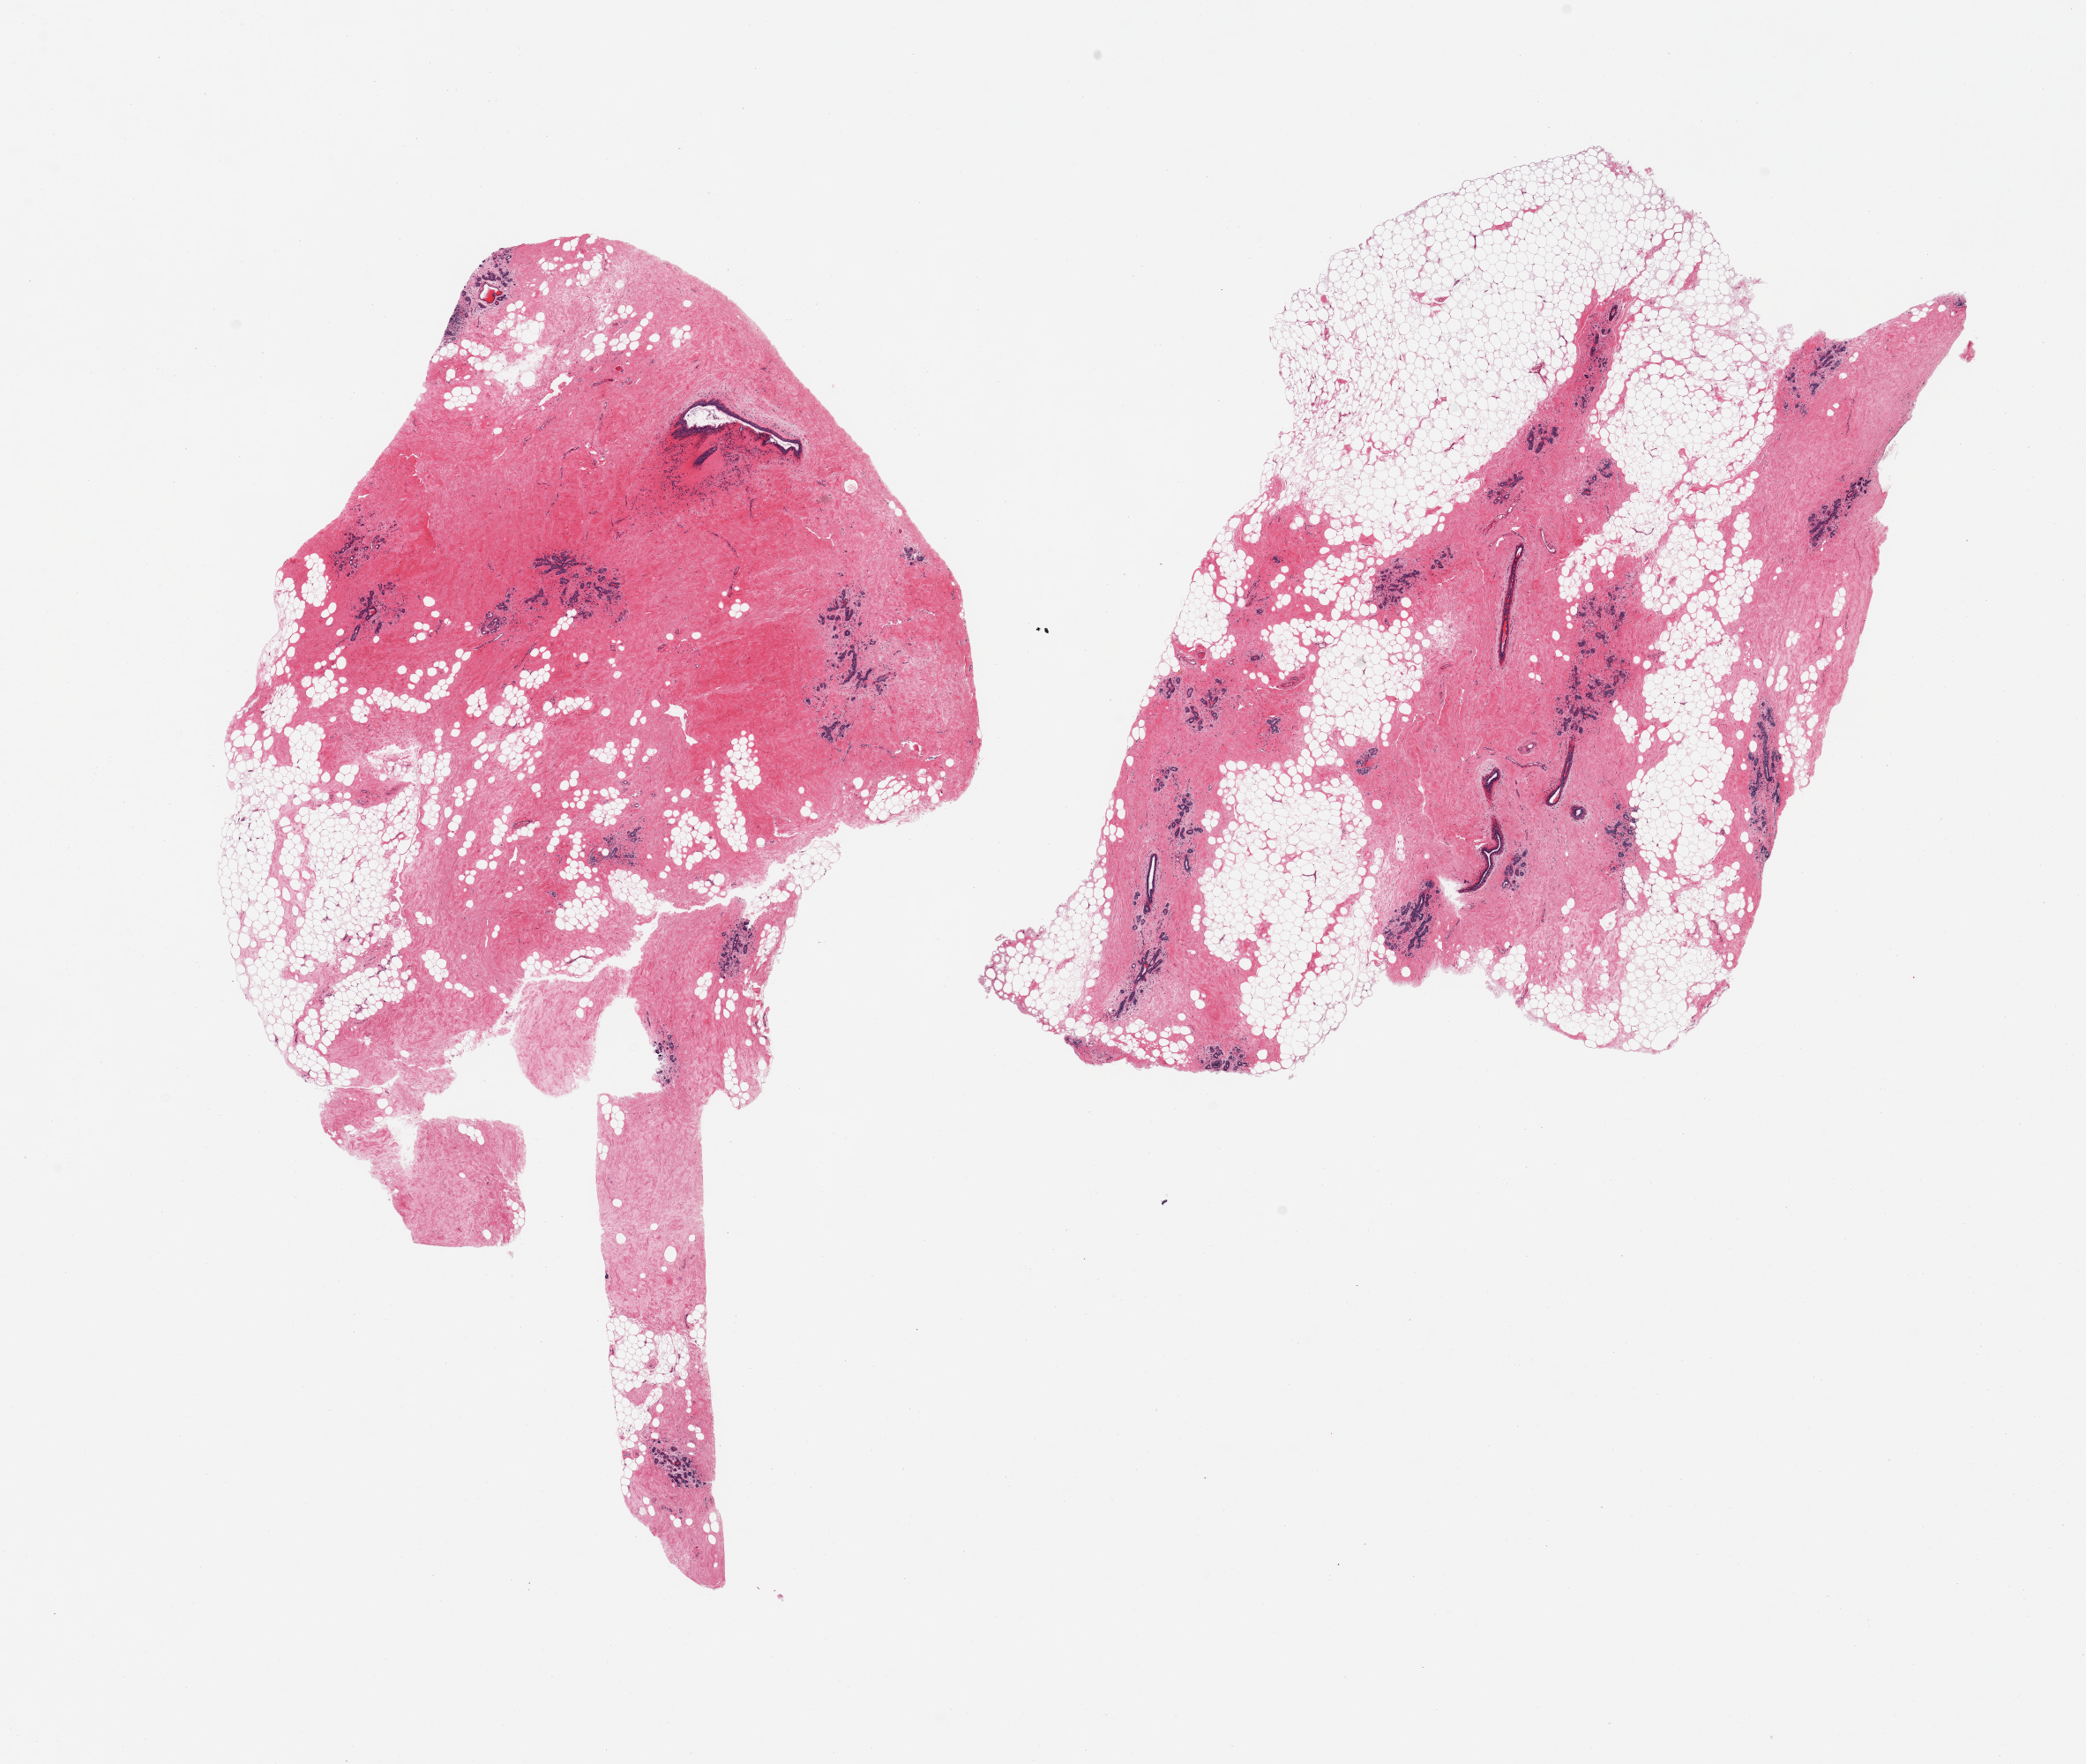
Whole-slide image, H&E stain — a low-resolution overview of the entire scanned area, about 18.7 x 15.8 mm. PAXgene-fixed paraffin-embedded (PFPE) section. Section of breast (target tissue). Tissue donor sample. Donor sex: female.
Review note (as recorded): 2 pieces; atrophic ductal and lobular units in fibroadipose tissue.